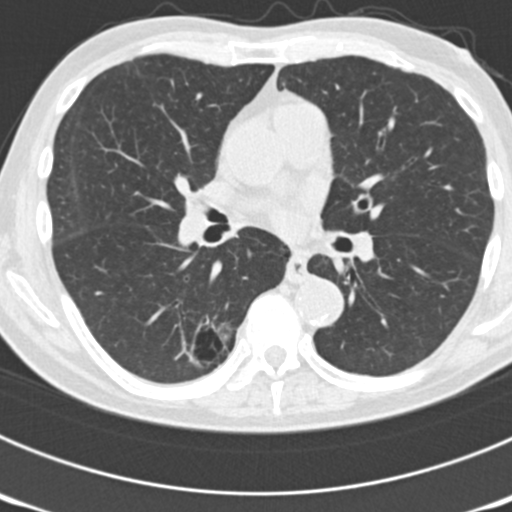
Axial slice from a low-dose chest CT screening exam. Third annual screen. Lung window (W 1500 / L -600 HU). 2 mm slice thickness. 120 kVp. Slice 78 of 177 in the series. 512 × 512 image matrix. Male participant, aged 70 years at enrolment. Current smoker at enrolment.
• Expert-annotated lung lesion, bounding box (x1, y1, x2, y2) in pixels: (146, 304, 237, 384).
• The screening reader recorded 3 non-calcified nodules or masses ≥4 mm on this exam (right upper lobe, left upper lobe, right lower lobe); which of them this box marks is not recorded.
• Later outcome: lung cancer diagnosed 14 days after this screen — bronchiolo-alveolar adenocarcinoma, NOS, right lower lobe, poorly differentiated (G3), stage IB (AJCC 6th edition), 30 mm at pathology.